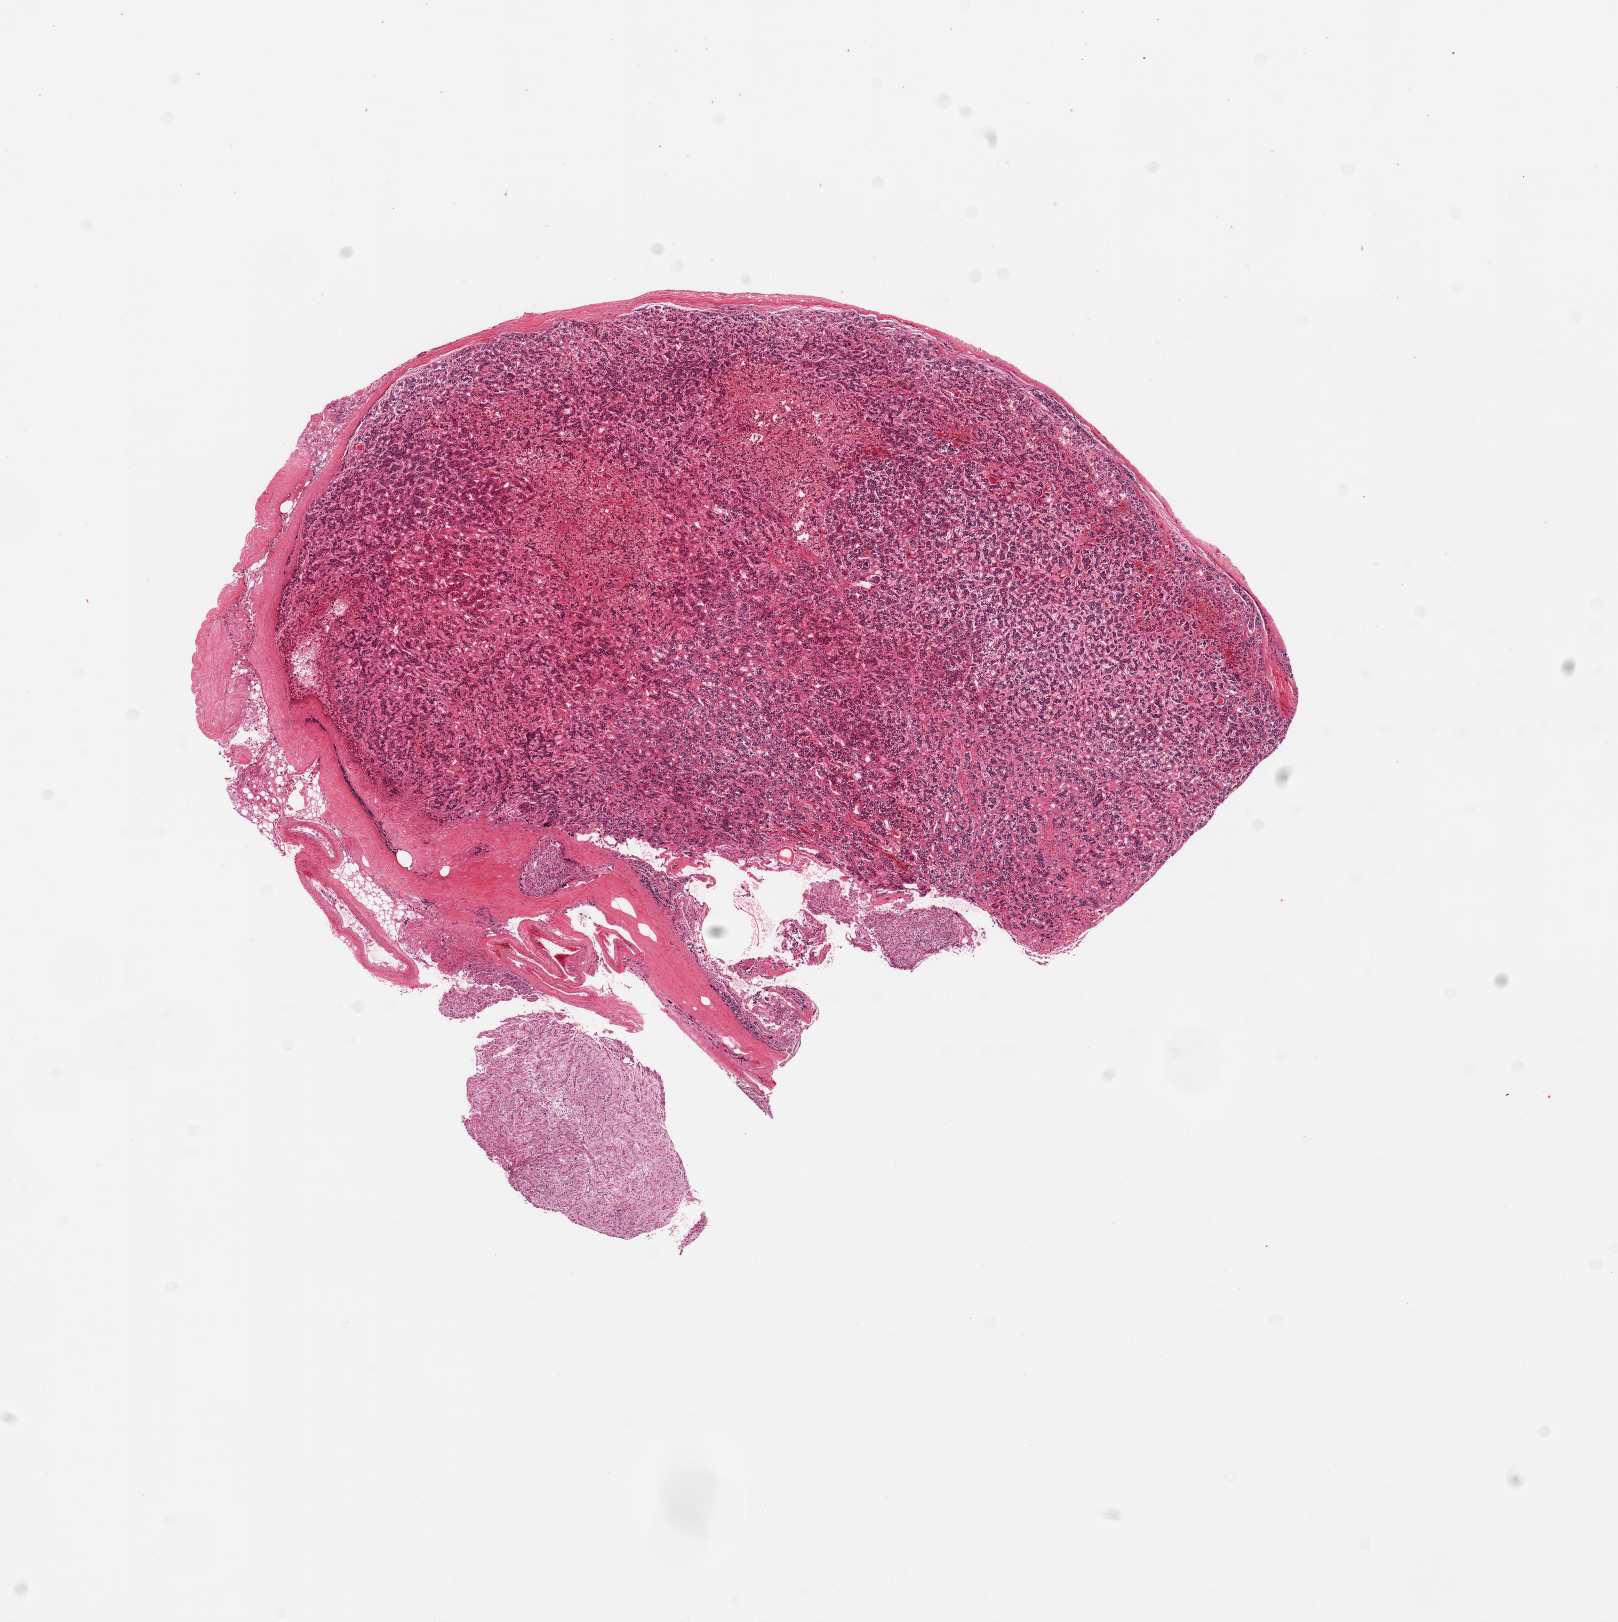
Digitized H&E-stained section, low-resolution overview of the scanned area, about 12.8 x 12.8 mm (from a 20x scan); PAXgene-fixed paraffin-embedded (PFPE) section; sampled site (target tissue): pituitary; donor tissue sample. Donor sex: male.
Pathologist's review note for this sample: 1 piece (fragmented); adenohypophysis with hemorrhage, dura, detached fragment of neurohypophysis.